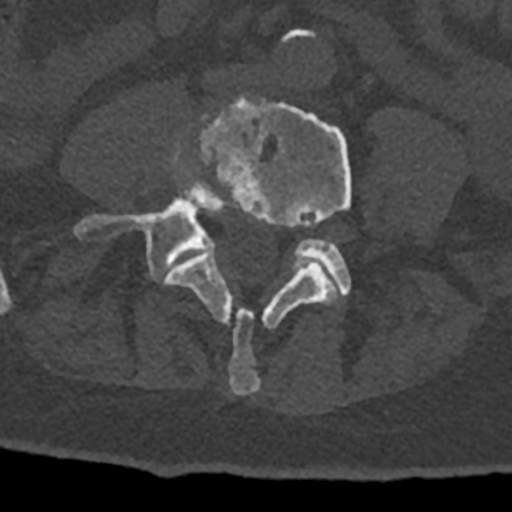
CT including the spine, one axial slice; position 235 of 797 along the scan axis; bone window (W 1800 / L 400 HU); 0.5 mm slice thickness; 512 × 512 image matrix, field of view 160 × 160 mm. Patient: male, 74 years. From the clinical record (not read from this slice): primary cancer: renal; vertebrae with lytic lesions (as recorded): T10, L1, L2, L3, L4, L5.
Structures marked on this image (semi-automatic segmentation, software-assisted and operator-edited):
- L4 vertebra: bounding box (x1, y1, x2, y2) in pixels: (165, 97, 351, 395)
- L5 vertebra: (73, 161, 351, 296)